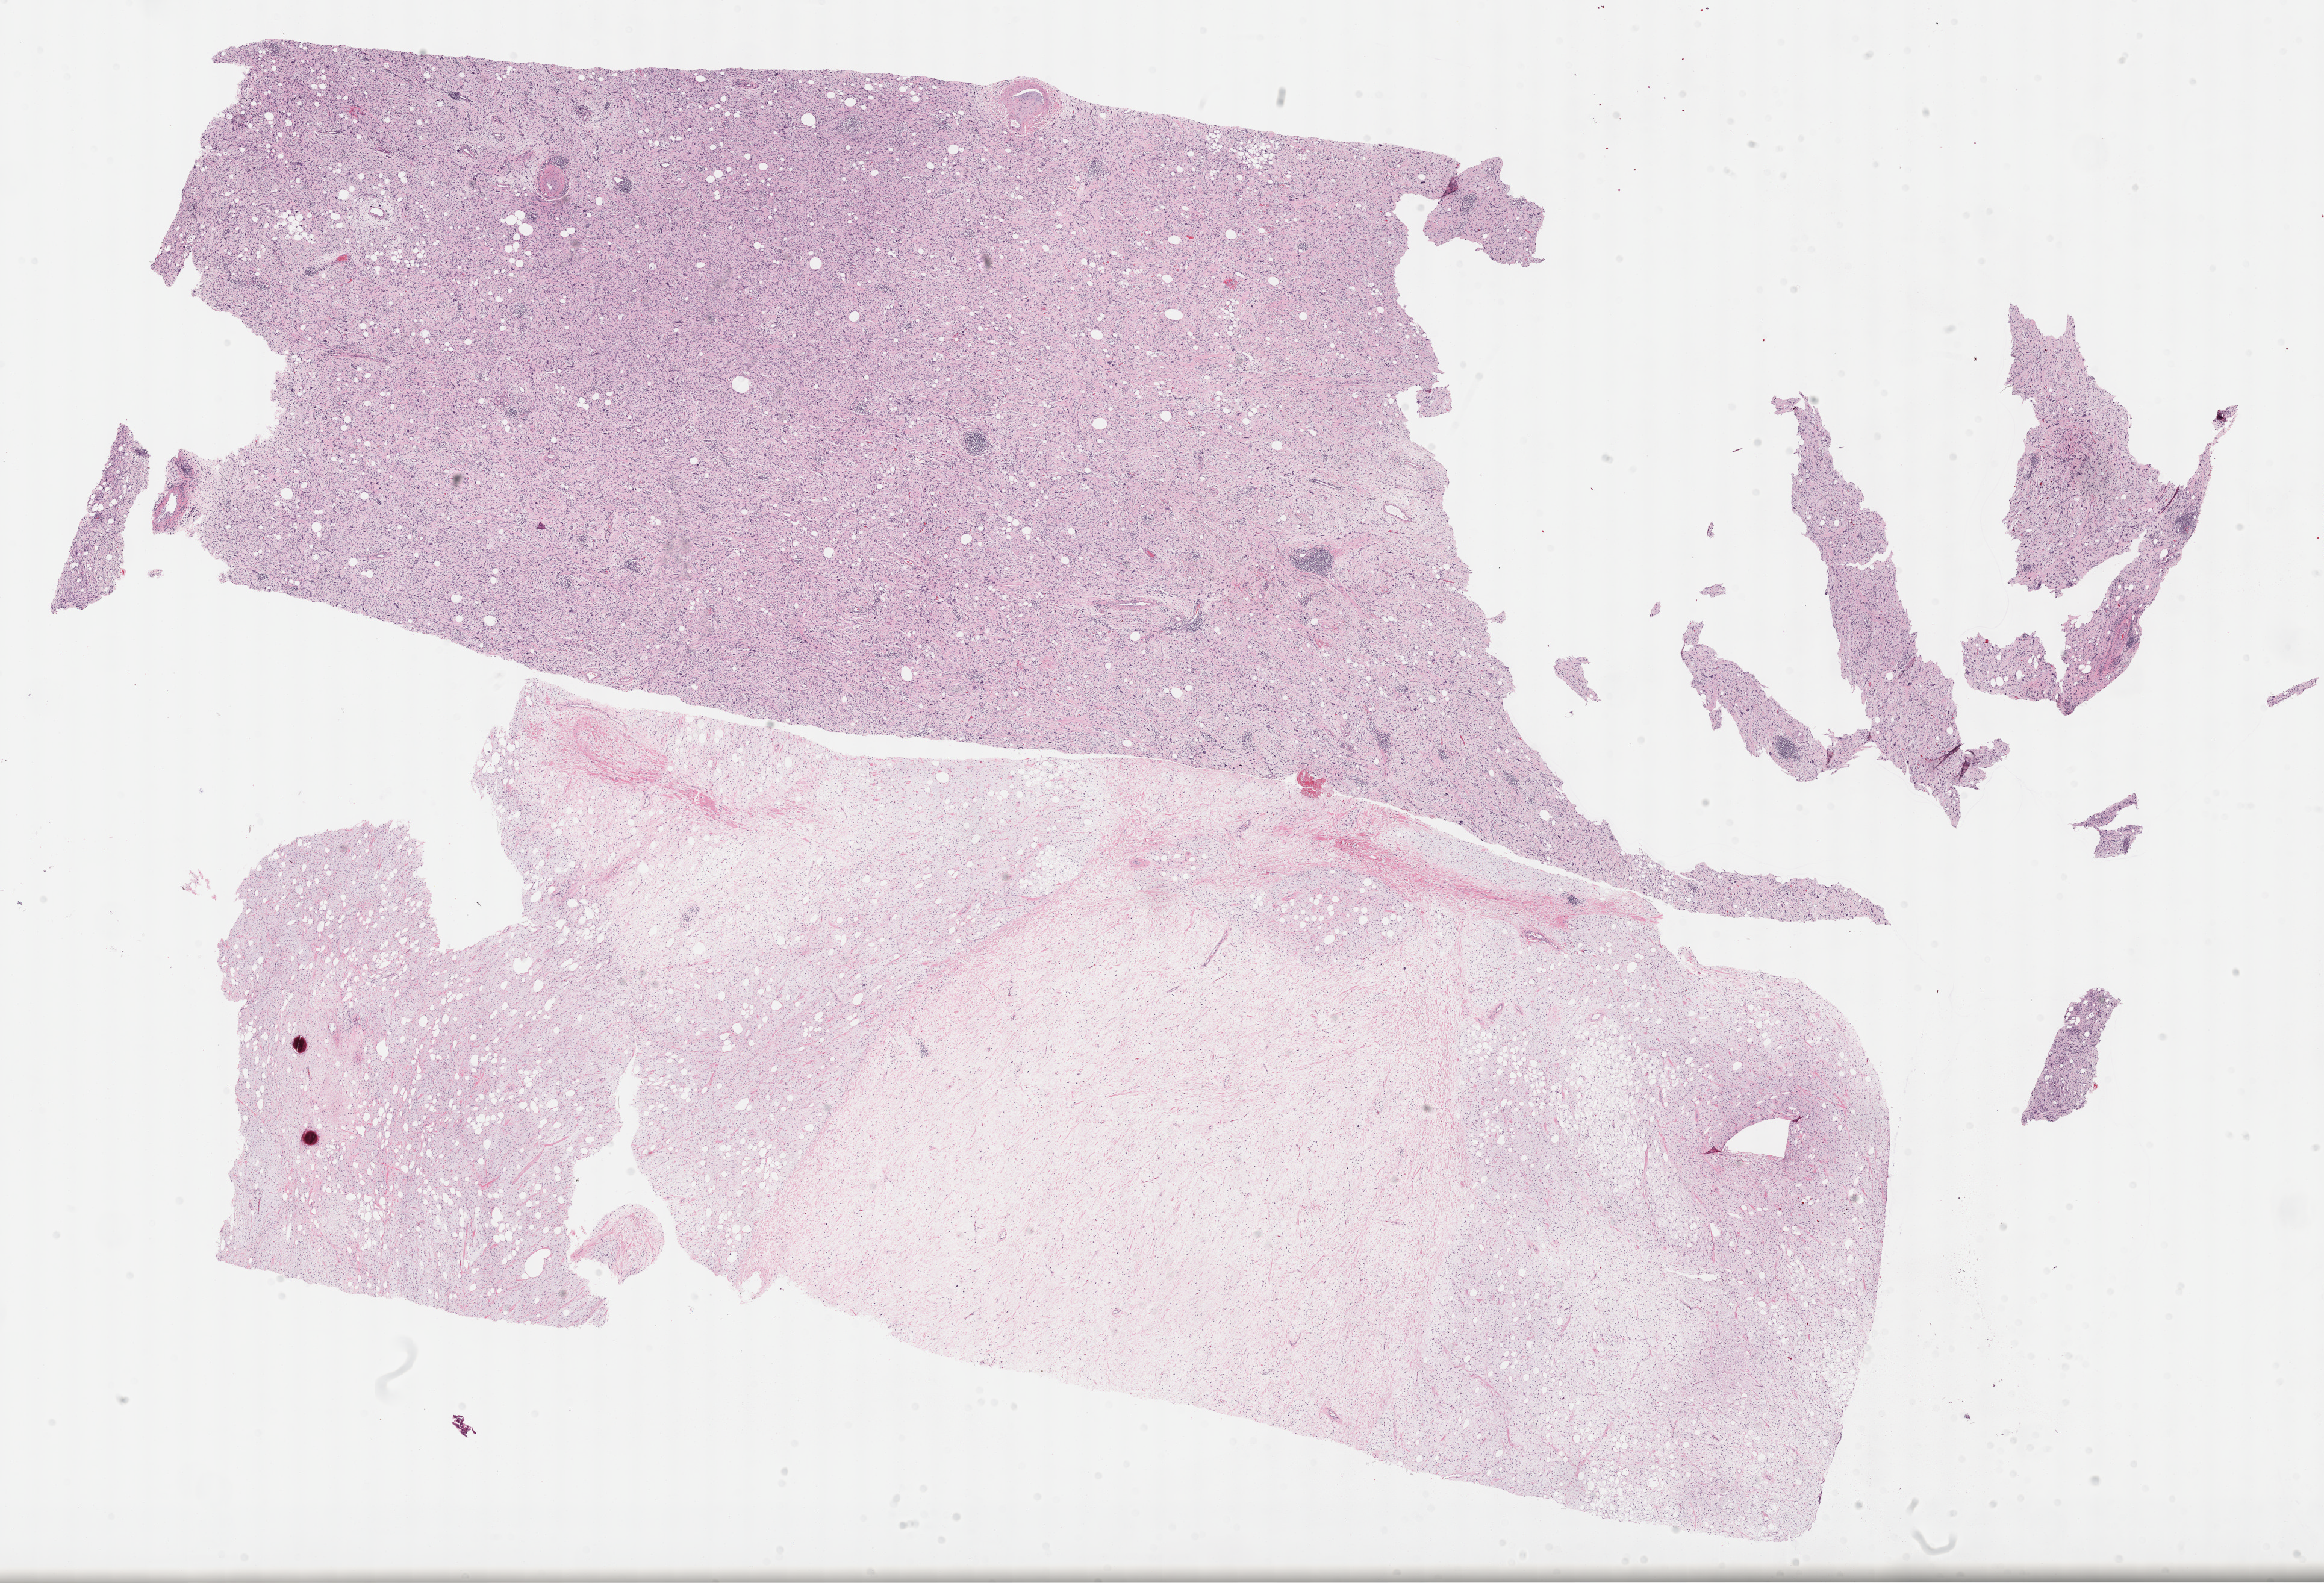
H&E whole-slide image — shown as a low-resolution overview of the whole scanned area (about 31.2 x 21.3 mm, from a 40x scan), formalin-fixed paraffin-embedded (FFPE) diagnostic section, sample: primary tumour, retroperitoneum and peritoneum. Patient: male, age at initial diagnosis 36 years.
- histologic diagnosis: Dedifferentiated liposarcoma (retroperitoneum)